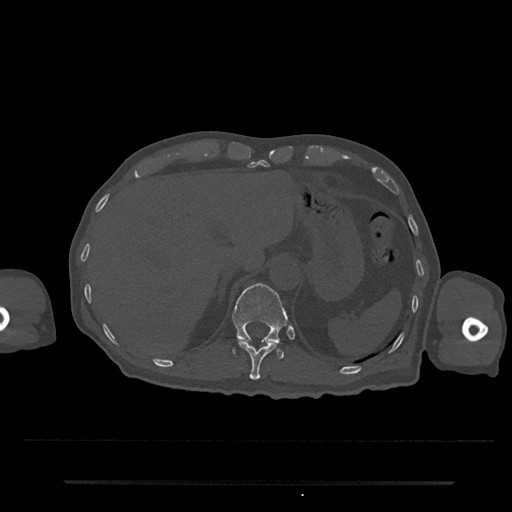
CT including the spine, one axial slice. Position 225 of 797 along the scan axis. 120 kVp. Bone window (W 1800 / L 400 HU). 0.5 mm slice thickness. 512 × 512 image matrix, field of view 427 × 427 mm. Patient: male, 74 years. Case-level facts recorded for this patient, not image findings: primary cancer: prostate.
Annotated regions visible in this slice (semi-automatically segmented with operator editing):
- T11 vertebra: bounding box [x1, y1, x2, y2] px = [237, 339, 278, 380]
- T12 vertebra: [232, 283, 288, 359]